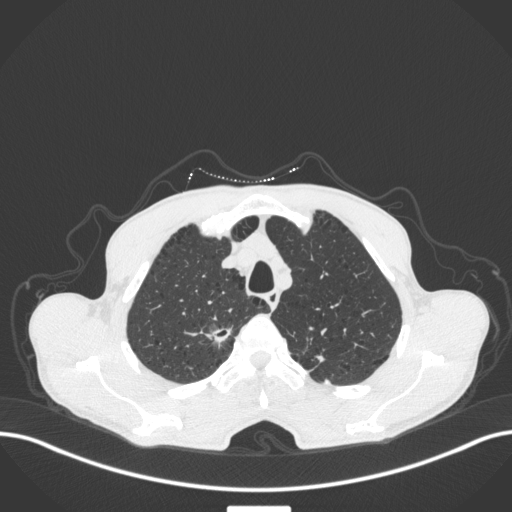
Chest CT, one axial slice. Position 355 of 445 along the scan axis. Reconstruction kernel B31f. 120 kVp. Lung window (W 1500 / L -600 HU). 1 mm slice thickness. 512 × 512 image matrix, field of view 400 × 400 mm. Patient: male, 70 years. From the clinical record (not read from this slice): clinical TNM (as recorded): T1a N0 M0; histopathological grade: G1-2.
Annotated regions visible in this slice (bounding box drawn by a radiologist):
- lung tumour (recorded histology: adenocarcinoma): bounding box [x1, y1, x2, y2] px = [204, 321, 238, 346]